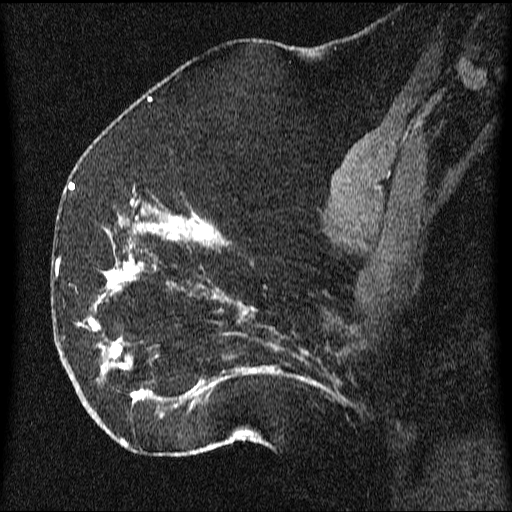
Breast MRI (dynamic contrast-enhanced), one sagittal slice; dynamic contrast-enhanced series, image 2 of 3 at this slice position (ordered by acquisition); 1.5 T; TE 4.2 ms, TR 9.1 ms; 512 × 512 image matrix, field of view 180 × 180 mm. Female patient, age 52 years.
Outlined on this slice (semi-automatic segmentation, software-assisted and operator-edited):
- analysis volume of interest (the breast-tissue region the enhancement analysis was run in; not a lesion): bounding box (x1, y1, x2, y2) in pixels: (61, 203, 350, 438)
- tumour enhancement mask (voxels above the 70 % enhancement threshold inside the analysis volume of interest): (78, 203, 324, 418)